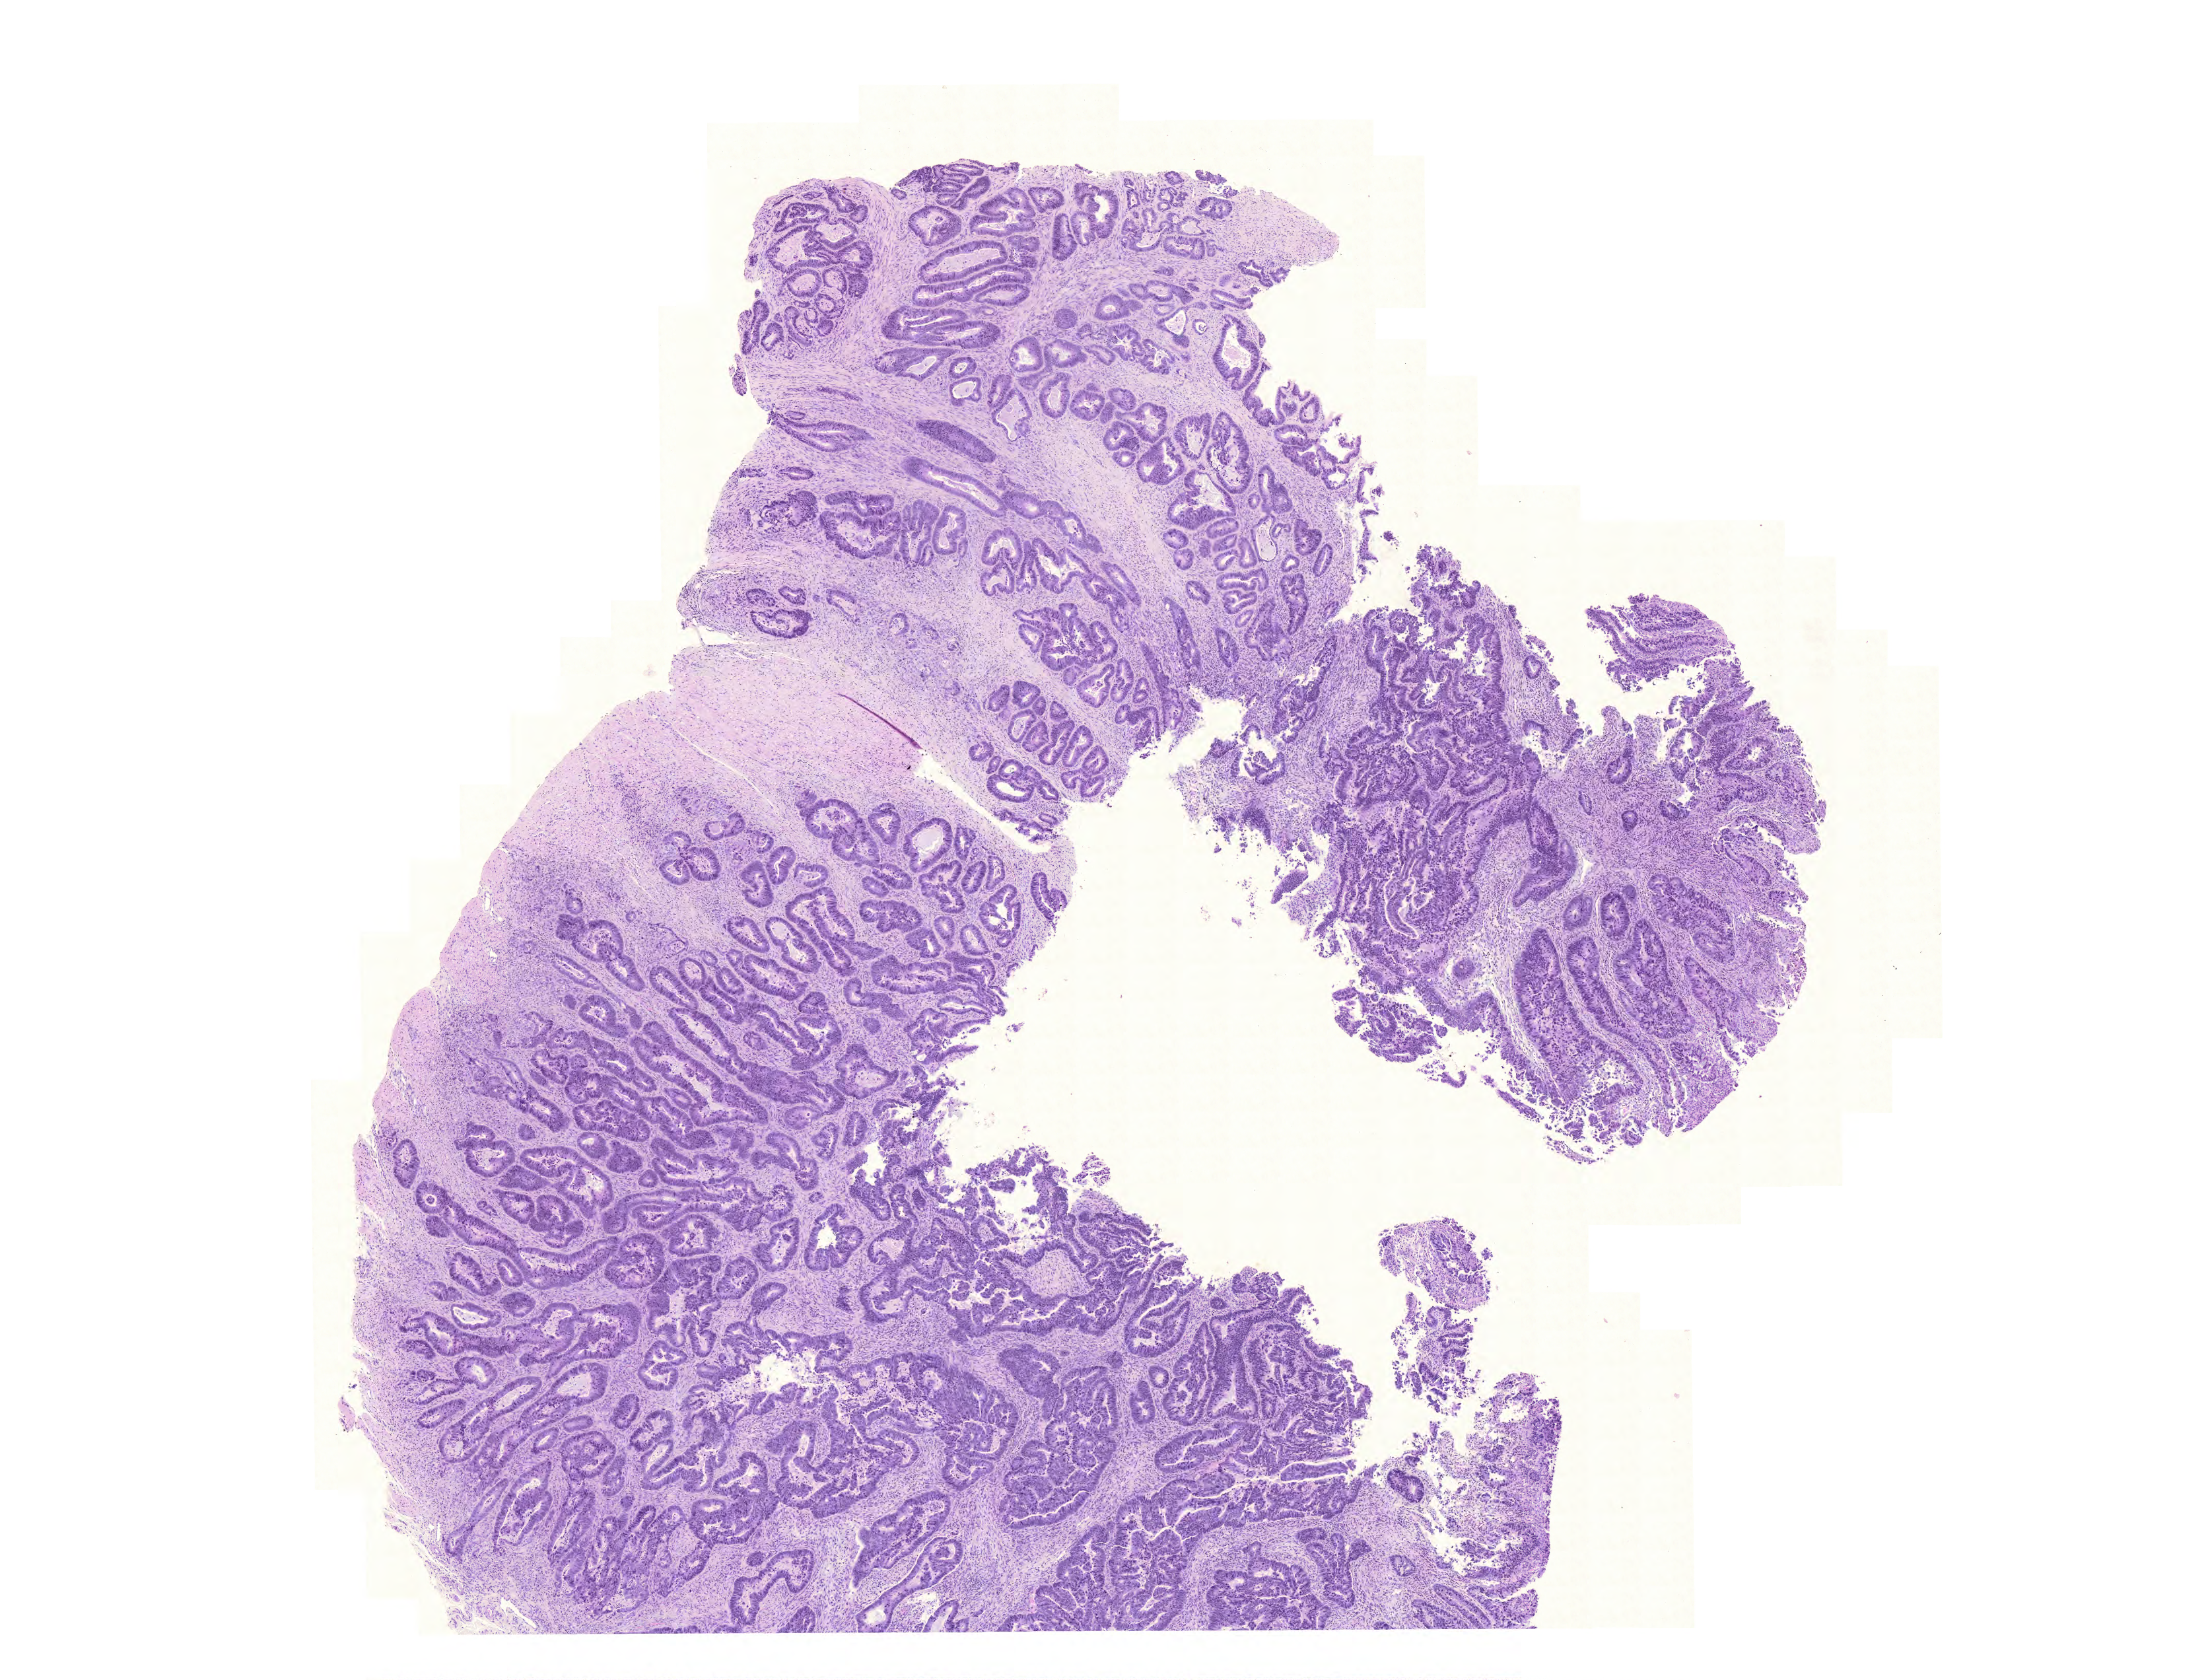
H&E-stained whole-slide image — whole scanned area (about 12.4 x 9.5 mm) shown as a low-resolution overview. Formalin-fixed paraffin-embedded (FFPE) diagnostic section. Rectum, primary tumour sample. Male, age 86 years at initial diagnosis.
Diagnosis: Adenocarcinoma, NOS (colon, NOS). TNM: T4 N2 M1. AJCC pathologic stage: IV (6th edition). Lymph nodes positive (case pathology): 5 of 34 examined.